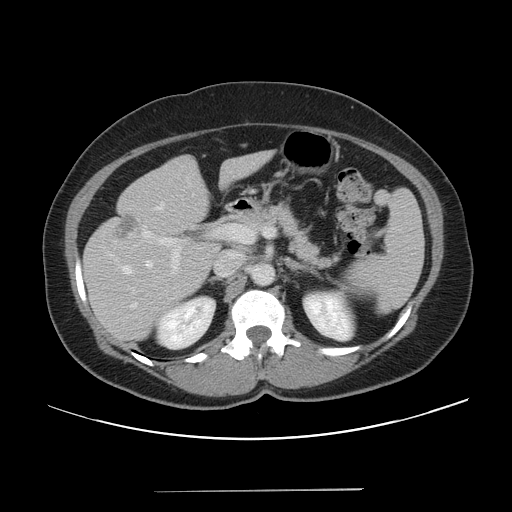
Contrast-enhanced abdominal CT, one axial slice. Position 25 of 56 along the scan axis. Soft-tissue window (W 400 / L 40 HU). 5 mm slice thickness. 512 × 512 image matrix, field of view 419 × 419 mm. Female patient, age 54 years. Case-level facts recorded for this patient, not image findings: diagnosis: colorectal cancer liver metastases, imaged before liver resection; multiple liver metastases: yes; largest metastasis: 3.2 cm; disease in both lobes: yes.
Outlined on this slice (expert manual segmentation):
- hepatic veins: box from (x=123, y=207) to (x=162, y=309) px
- liver: (x=83, y=152)–(x=271, y=343)
- planned liver remnant (the part of the liver to remain after resection): (x=167, y=152)–(x=271, y=210)
- portal vein (with intrahepatic branches): (x=144, y=225)–(x=274, y=271)
- liver metastasis: (x=116, y=214)–(x=138, y=239)